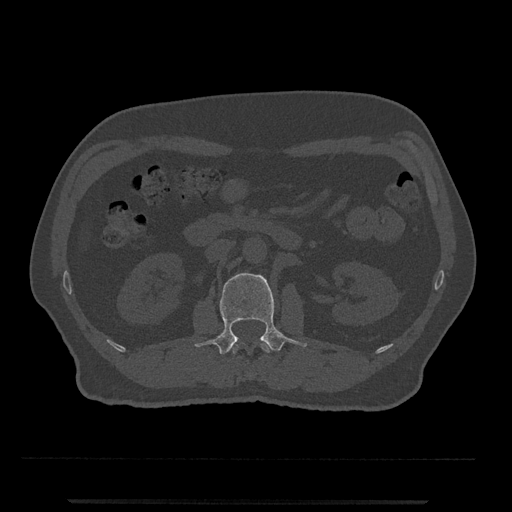
CT including the spine, one axial slice; 120 kVp; bone window (W 1800 / L 400 HU); 0.5 mm slice thickness; 512 × 512 image matrix, field of view 419 × 419 mm. Patient: male, 63 years. From the clinical record (not read from this slice): primary cancer: prostate.
Outlined on this slice (semi-automatic segmentation, software-assisted and operator-edited):
- L1 vertebra: box from (x=230, y=341) to (x=270, y=354) px
- L2 vertebra: (x=195, y=273)–(x=307, y=355)